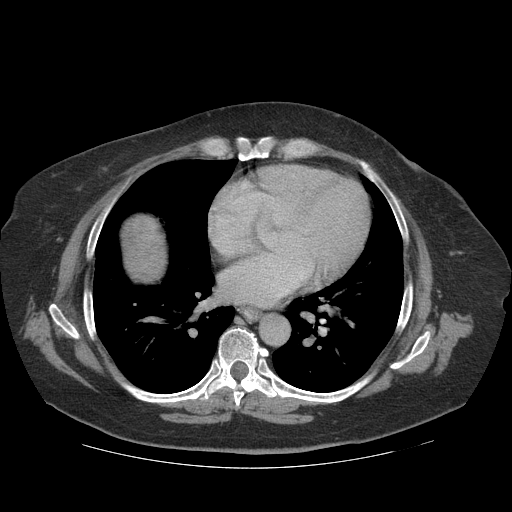
Contrast-enhanced abdominal CT (liver protocol), one axial slice. Reconstruction kernel STANDARD. Soft-tissue window (W 400 / L 40 HU). 512 × 512 image matrix. From the clinical record (not read from this slice): diagnosis: hepatocellular carcinoma (patient treated with transarterial chemoembolisation; whether this scan precedes or follows treatment is not stated here); TNM stage (as recorded): Stage-IIIA; Child-Pugh class: A.
Outlined on this slice (semi-automatically segmented with operator editing):
- liver parenchyma outside the tumour (the mass and vessels are separate outlines, so this box may not span the whole liver): box from (x=122, y=214) to (x=166, y=280) px